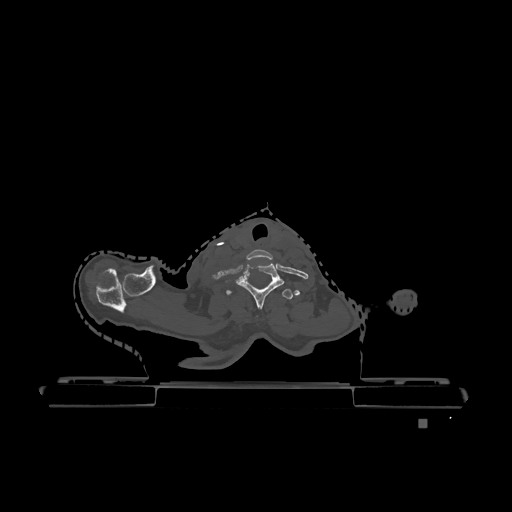
CT including the spine, one axial slice. Slice 1025 of 1317 in the series (ordered by position). Bone window (W 1800 / L 400 HU). 0.5 mm slice thickness. 512 × 512 image matrix, field of view 500 × 500 mm. Patient: female, 74 years. Case-level facts recorded for this patient, not image findings: primary cancer: lung; vertebrae with lytic lesions (as recorded): T1, T4, T5, T6, L4, L5.
Annotated regions visible in this slice (semi-automatically segmented with operator editing):
- T1 vertebra: bounding box [x1, y1, x2, y2] px = [226, 289, 293, 299]